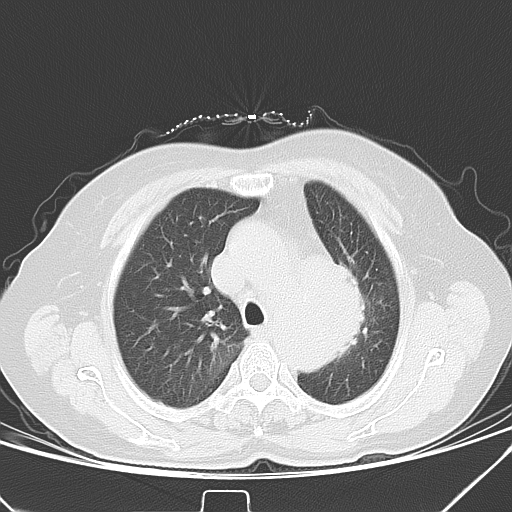
Chest CT, one axial slice; slice 30 of 40 in the series (ordered by position); 120 kVp; lung window (W 1500 / L -600 HU); 512 × 512 image matrix, field of view 331 × 331 mm. Patient: female, 59 years. Case-level facts recorded for this patient, not image findings: clinical TNM (as recorded): T3 N1 M0.
Structures marked on this image (rectangle marked by the reading radiologist):
- lung tumour (recorded histology: small cell carcinoma): bounding box (x1, y1, x2, y2) in pixels: (333, 251, 373, 365)